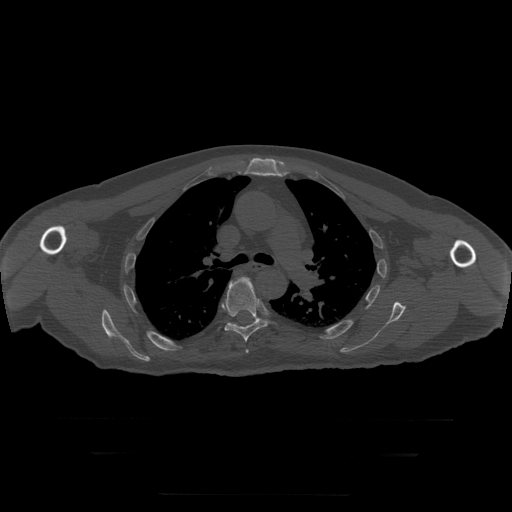
CT including the spine, one axial slice. Position 208 of 397 along the scan axis. Reconstruction kernel STANDARD. 120 kVp. Bone window (W 1800 / L 400 HU). 1.25 mm slice thickness. 512 × 512 image matrix, field of view 510 × 510 mm. Patient age 73 years. From the clinical record (not read from this slice): primary cancer: prostate.
Structures marked on this image (semi-automatically segmented with operator editing):
- T5 vertebra: box from (x=246, y=350) to (x=249, y=353) px
- T6 vertebra: (x=225, y=277)–(x=268, y=343)
- T7 vertebra: (x=254, y=316)–(x=257, y=320)